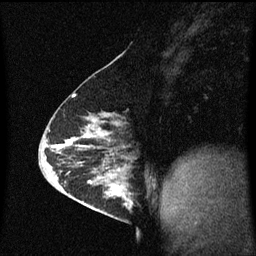
Breast MRI (dynamic contrast-enhanced), one sagittal slice. Dynamic contrast-enhanced series, image 2 of 3 at this slice position (ordered by acquisition). 1.5 T. TE 4.2 ms, TR 8.4 ms. 2 mm slice thickness. 256 × 256 image matrix. Patient: female, 63 years.
Outlined on this slice (semi-automatic segmentation, software-assisted and operator-edited):
- analysis volume of interest (the breast-tissue region the enhancement analysis was run in; not a lesion): bounding box <98,168,135,217> (left, top, right, bottom; pixels)
- tumour enhancement mask (voxels above the 70 % enhancement threshold inside the analysis volume of interest): <98,168,133,211>